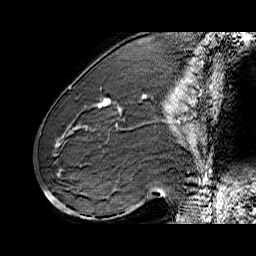
Breast MRI (dynamic contrast-enhanced), one sagittal slice. Dynamic contrast-enhanced series, time point 2 of 6 at this slice position (early post-contrast). 1.5 T. TE 6.4 ms, TR 32.9 ms. 4 mm slice thickness. 256 × 256 image matrix. Female patient. Case-level facts recorded for this patient, not image findings: setting: breast cancer imaged before/during neoadjuvant chemotherapy; receptor status: HER2-positive.
Structures marked on this image (semi-automatically segmented with operator editing):
- analysis volume of interest (the breast-tissue region the enhancement analysis was run in; not a lesion): bounding box [x1, y1, x2, y2] px = [71, 80, 155, 146]
- tumour enhancement mask (voxels above the 100 % enhancement threshold inside the analysis volume of interest): [99, 99, 121, 109]